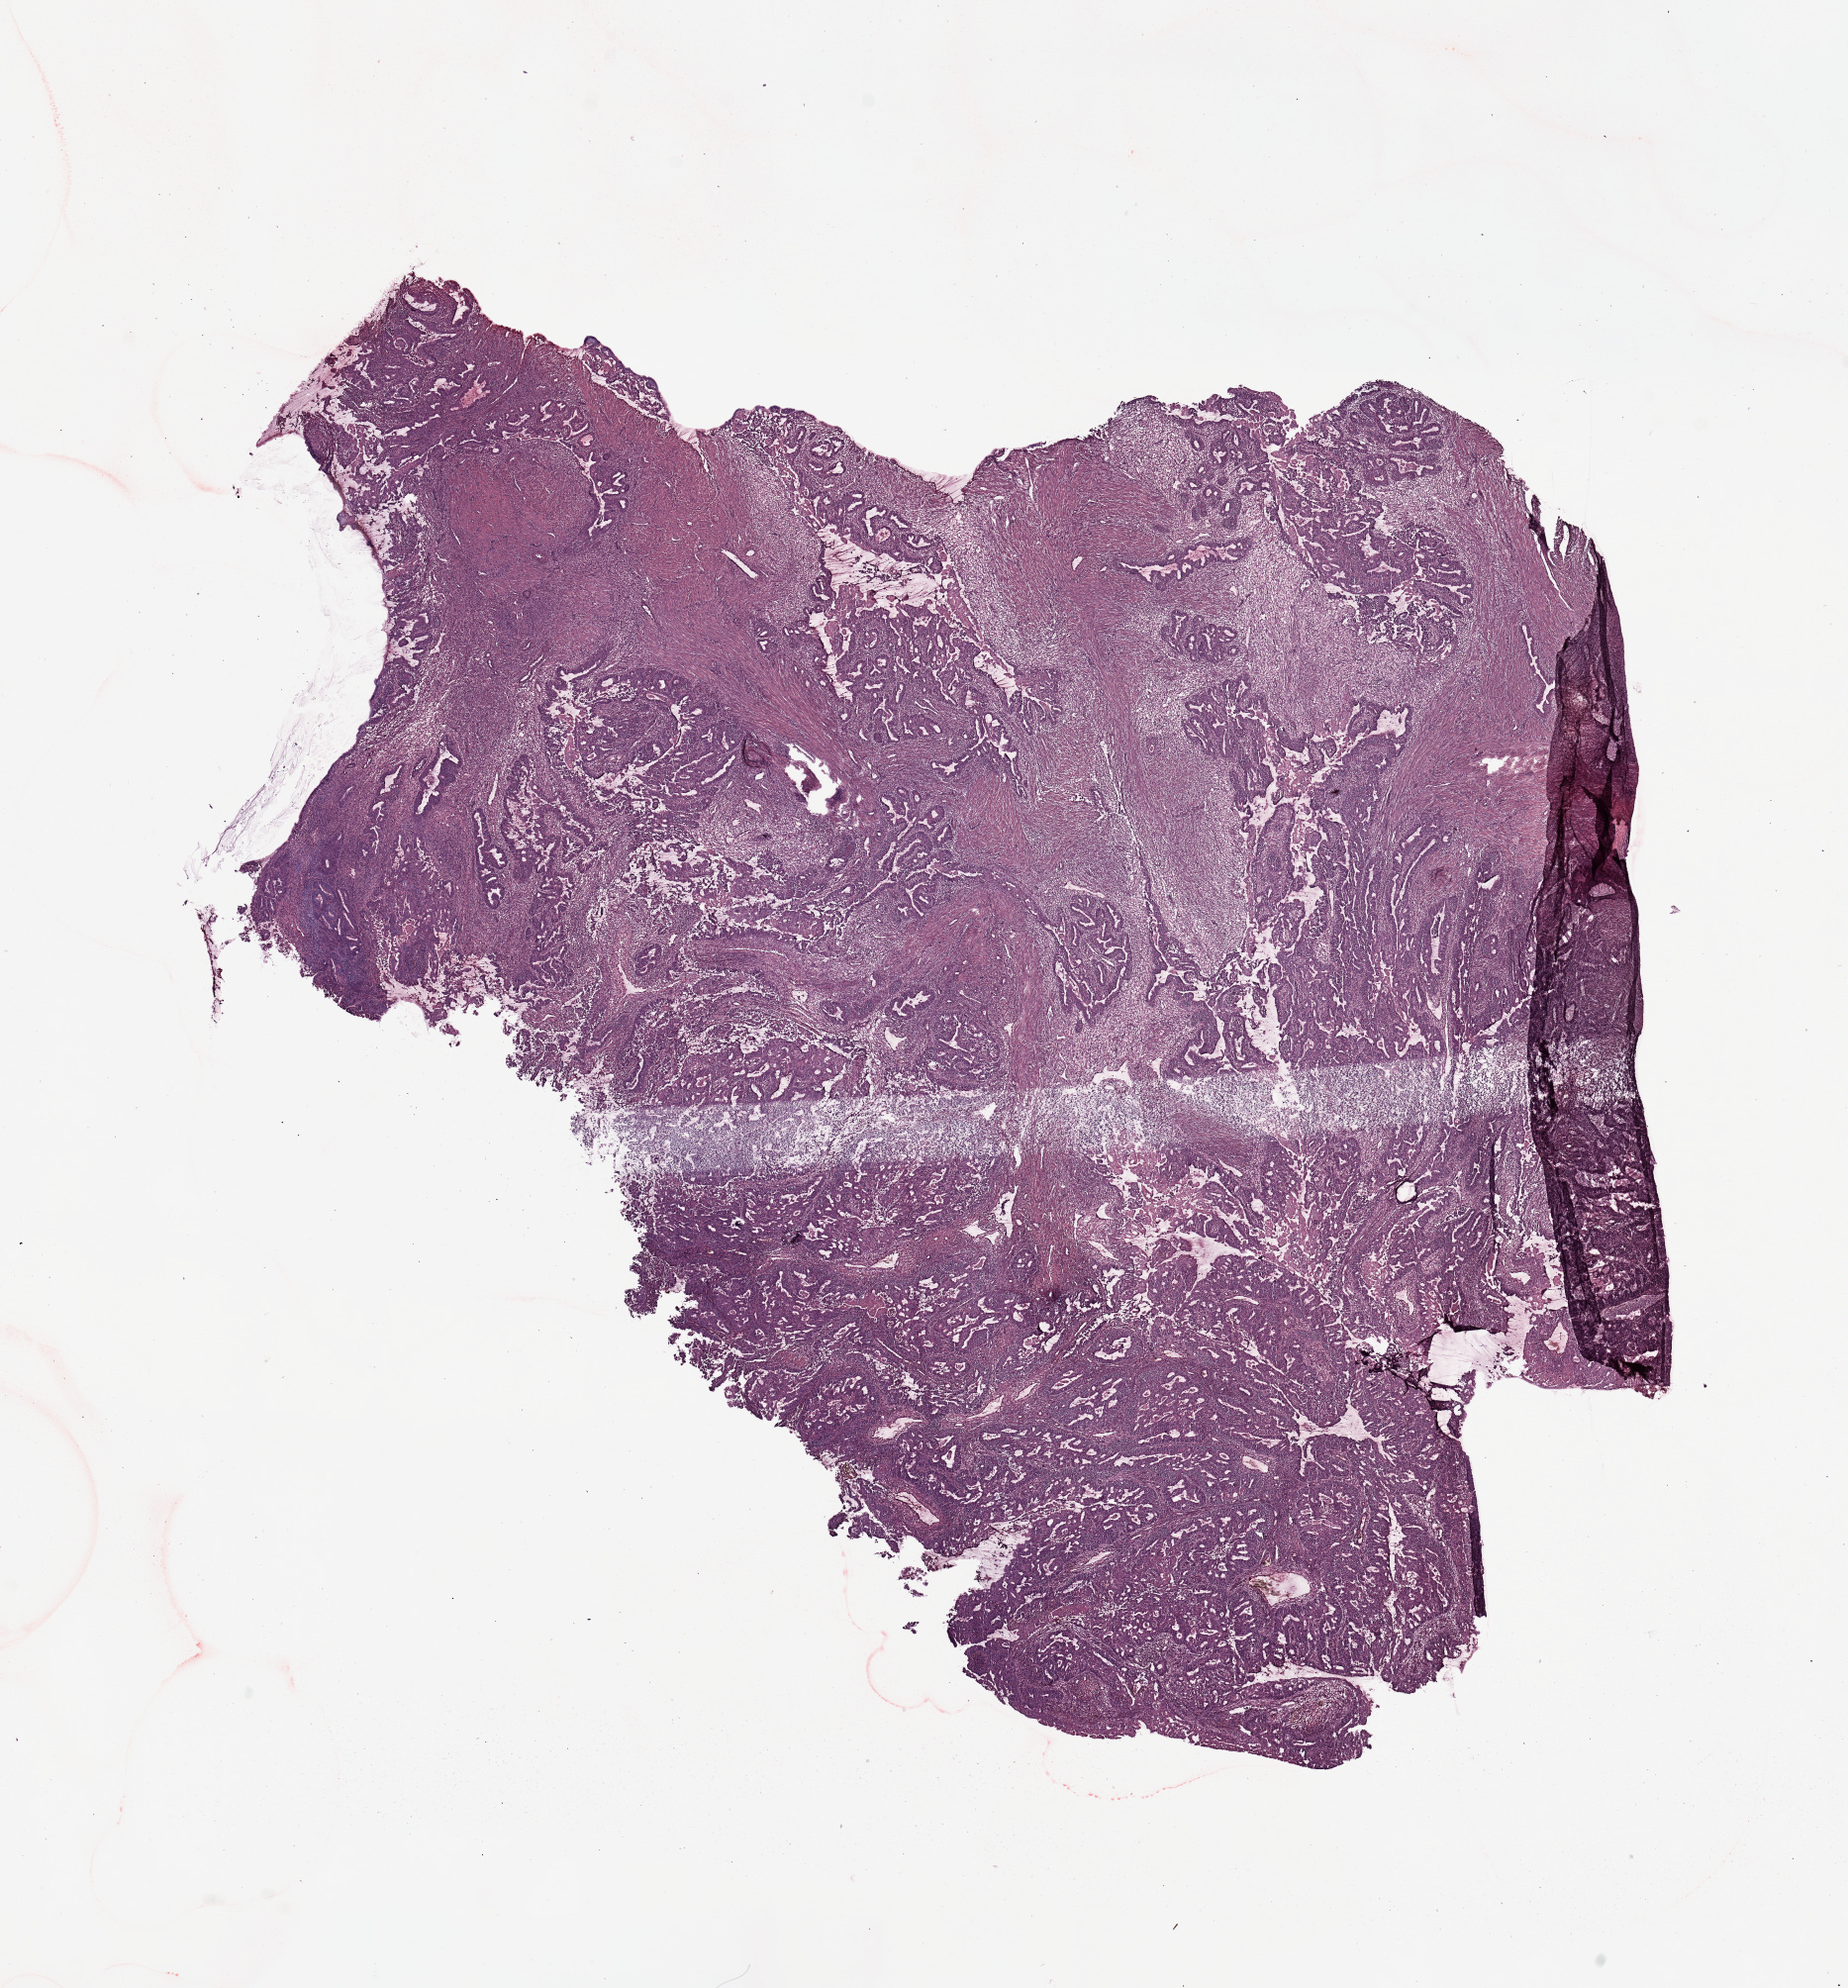
Hematoxylin and eosin (H&E) stained whole-slide image — a low-resolution overview of the entire scanned area, about 14.8 x 15.9 mm (slide scanned at 20x), tumour tissue sample, uterus. Female, 41 y/o. Histologic grade: G2 (moderately differentiated).
Diagnosis: Endometrioid adenocarcinoma, NOS. AJCC pathologic stage: I.